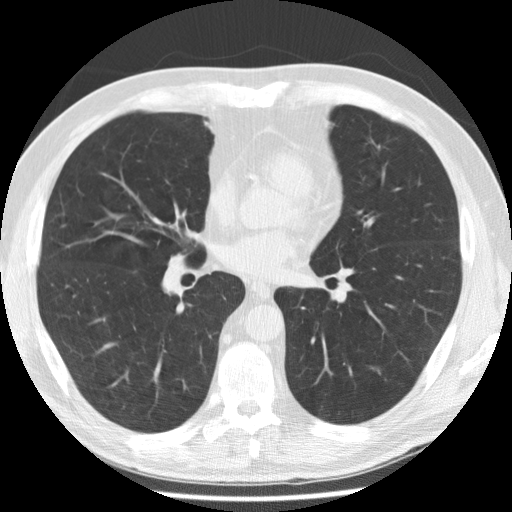
Axial slice from a low-dose chest CT screening exam. Second annual screen. Lung window (W 1500 / L -600 HU). 2.5 mm slice thickness. Standard (soft-tissue) reconstruction kernel (STANDARD). 120 kVp. Slice 136 of 260 in the series. 512 × 512 image matrix. Male participant, aged 58 years at enrolment. Former smoker at enrolment.
- Expert-annotated lung lesion, bounding box [x1, y1, x2, y2] px = [356, 350, 393, 385].
- The exam's reader record, not a measurement of the box and not confirmed to be the same lesion: non-calcified nodule or mass ≥4 mm, left lower lobe, 7 × 4 mm, poorly defined margins, ground glass attenuation, pre-existing on the prior screen: yes; interval growth: yes.
- Later outcome: lung cancer diagnosed 407 days after this screen — adenocarcinoma, NOS, left lower lobe, poorly differentiated (G3), stage IA (AJCC 6th edition), 8 mm at pathology.